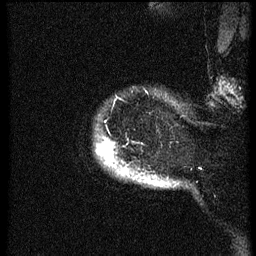
Breast MRI (dynamic contrast-enhanced), one sagittal slice. Dynamic contrast-enhanced series, image 2 of 3 at this slice position (ordered by acquisition). 1.5 T. TE 4.2 ms, TR 8.4 ms. 256 × 256 image matrix, field of view 200 × 200 mm. Female patient, age 38 years. From the clinical record (not read from this slice): setting: breast cancer imaged before/during neoadjuvant chemotherapy; receptor status: HER2-positive.
Outlined on this slice (semi-automatic segmentation, software-assisted and operator-edited):
- analysis volume of interest (the breast-tissue region the enhancement analysis was run in; not a lesion): bounding box [x1, y1, x2, y2] px = [98, 129, 173, 188]
- tumour enhancement mask (voxels above the 70 % enhancement threshold inside the analysis volume of interest): [99, 146, 124, 175]